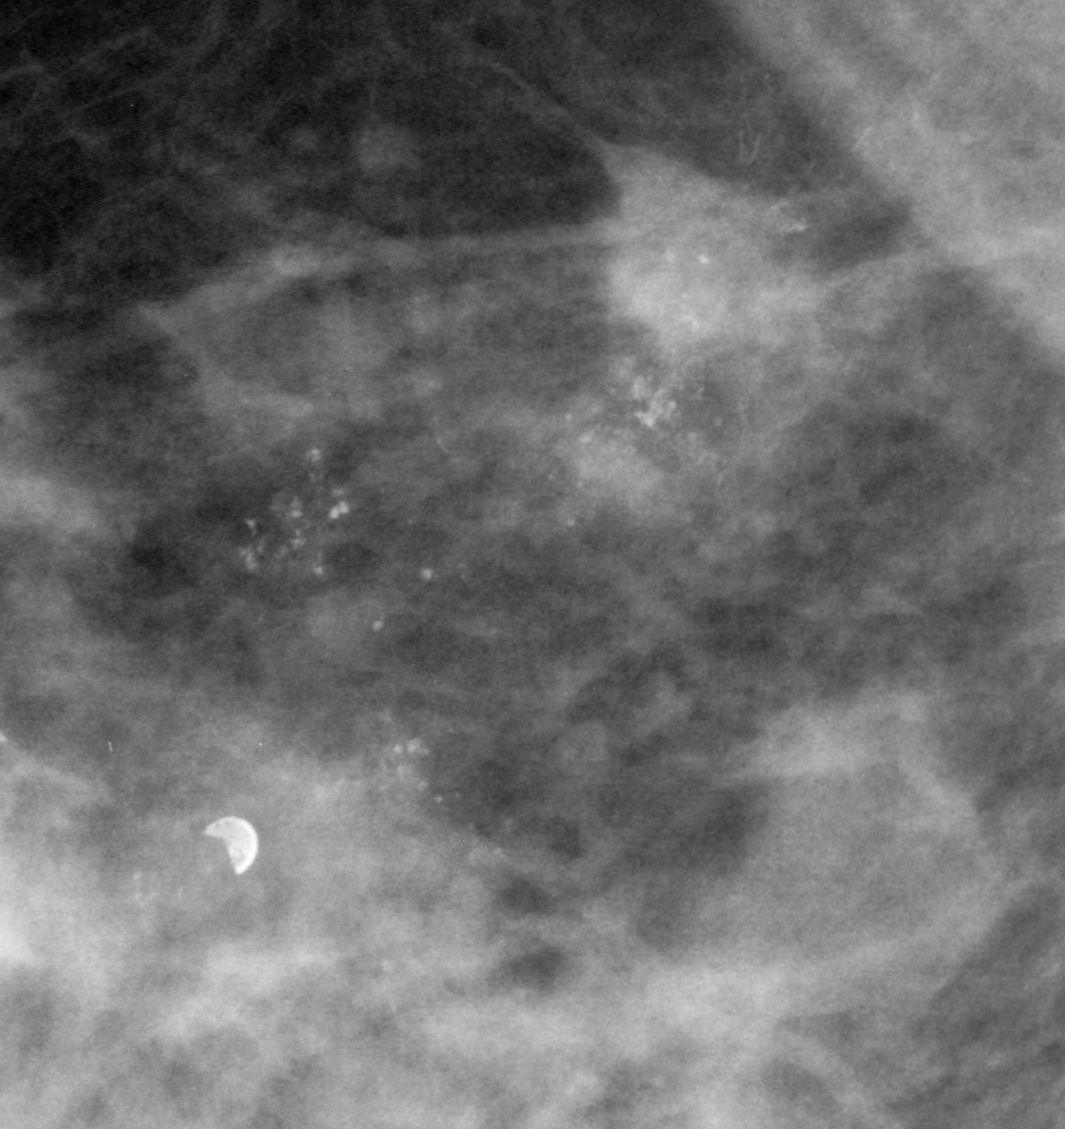
Crop from a digitized film mammogram around one marked abnormality; left breast; MLO view; BI-RADS breast density category 4 (scale 1–4).
Calcifications, morphology pleomorphic, distribution regional; BI-RADS assessment category 5; subtlety rating 5 on a 1 (subtle) to 5 (obvious) scale; pathology result (as recorded, not read from the image): malignant.